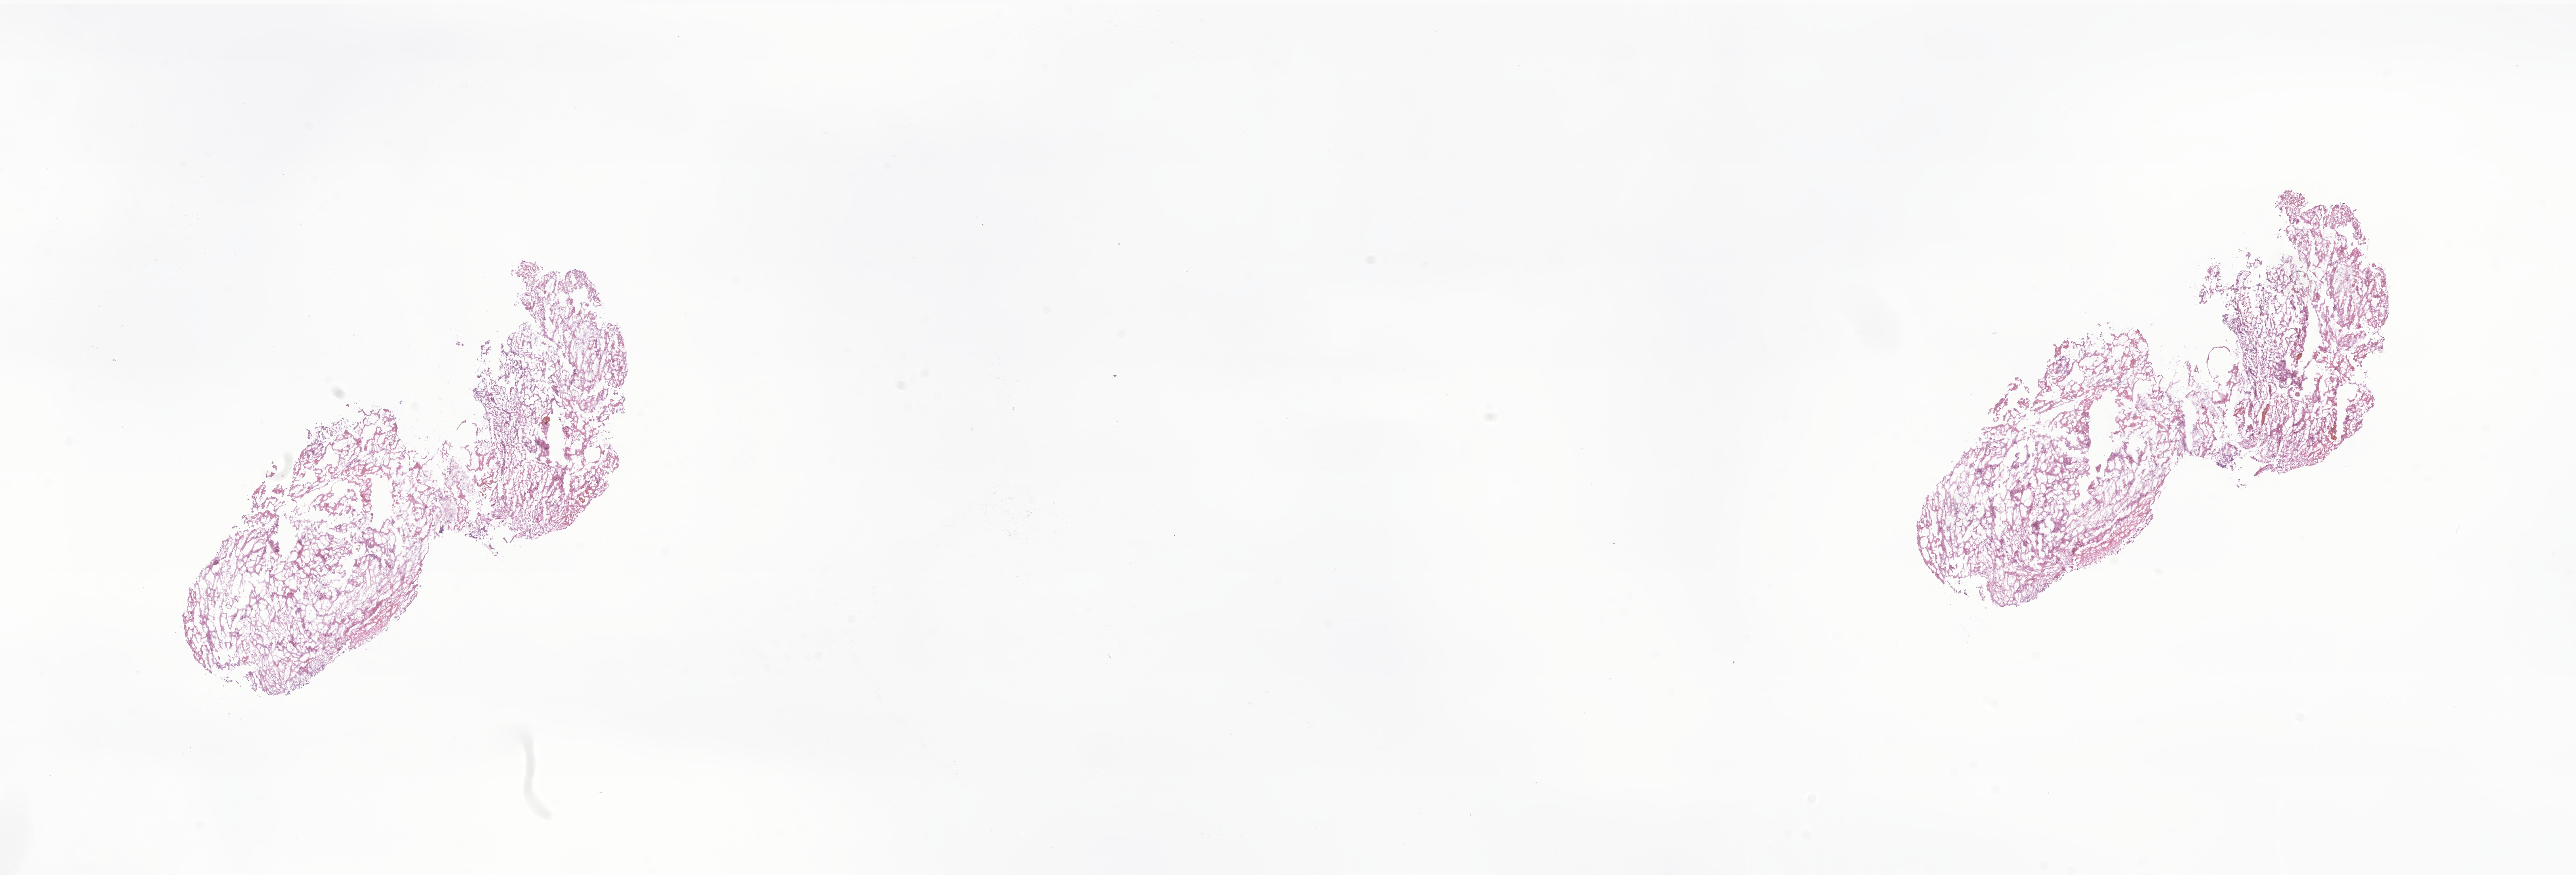
H&E whole-slide image of tumor tissue from the brain stem, a low-resolution overview of the entire scanned area, about 26.9 x 9.1 mm. Frozen section. Patient: male, age 104 months (8 years 8 months).
Diagnosis (ICD-O-3 morphology term): Pilocytic astrocytoma.